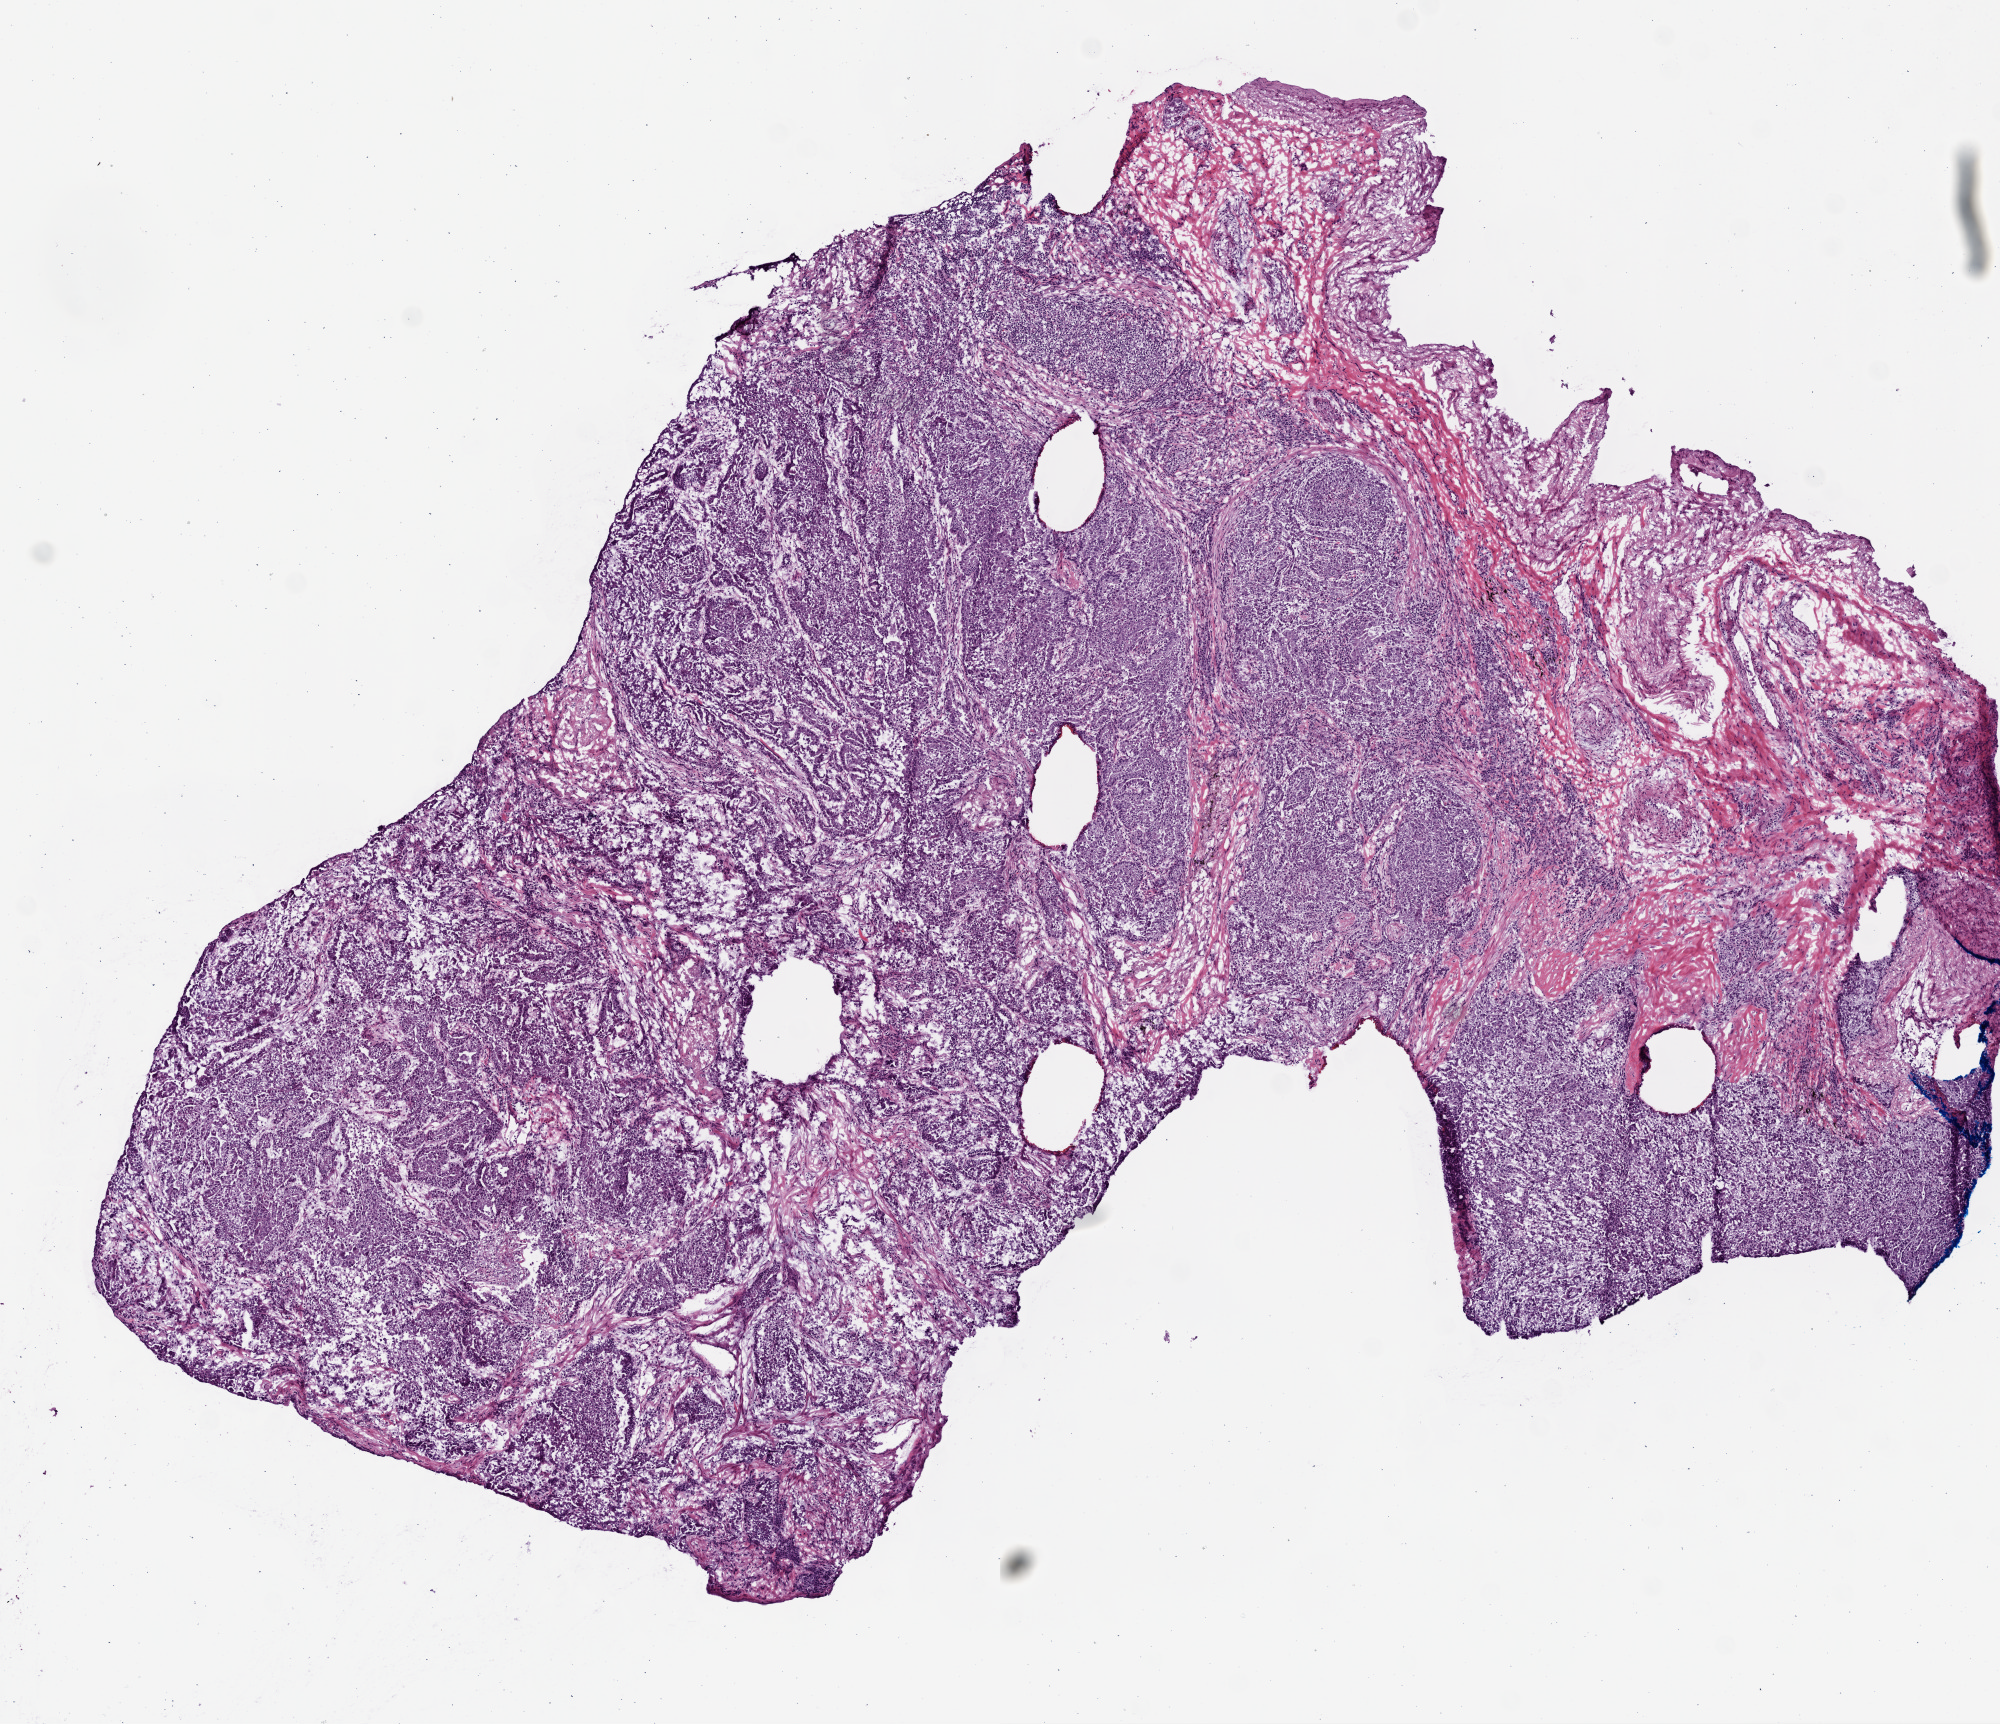
H&E whole-slide image — whole scanned area (about 8.0 x 6.9 mm, slide scanned at 20x) shown as a low-resolution overview. Frozen section from the top of the tissue portion. Primary tumour sample from the lung. Male, age 64 years at initial diagnosis. Composition of this section per pathologist review: tumour cells 80%, tumour nuclei 80%, normal cells 0%, stromal cells 20%, necrosis 0%.
AJCC pathologic stage: IA. Pathologic diagnosis: Papillary adenocarcinoma, NOS. TNM: T1b N0 M0.